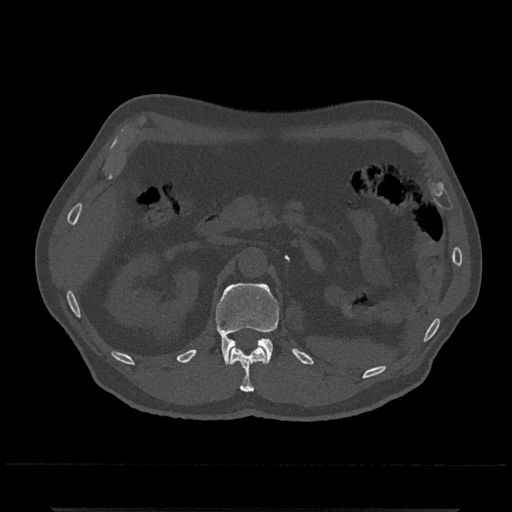
CT including the spine, one axial slice. Slice 388 of 797 in the series (ordered by position). 120 kVp. Bone window (W 1800 / L 400 HU). 0.5 mm slice thickness. 512 × 512 image matrix, field of view 393 × 393 mm. Male patient, age 67 years. From the clinical record (not read from this slice): primary cancer: prostate.
Structures marked on this image (semi-automatic segmentation, software-assisted and operator-edited):
- L1 vertebra: box from (x=216, y=283) to (x=279, y=365) px
- T12 vertebra: (x=229, y=346)–(x=267, y=392)